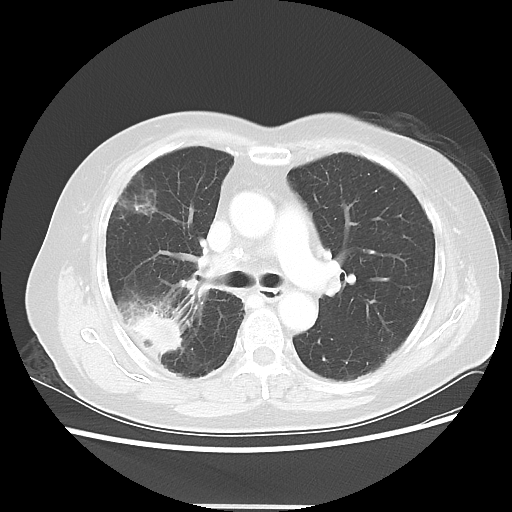
Chest CT, one axial slice; 120 kVp; lung window (W 1500 / L -600 HU); 512 × 512 image matrix, field of view 360 × 360 mm. Female patient, age 72 years. From the clinical record (not read from this slice): clinical TNM (as recorded): T2 N1 M0; histopathological grade: G1.
Outlined on this slice (bounding box drawn by a radiologist):
- lung tumour (recorded histology: adenocarcinoma): bounding box (x1, y1, x2, y2) in pixels: (126, 309, 184, 354)